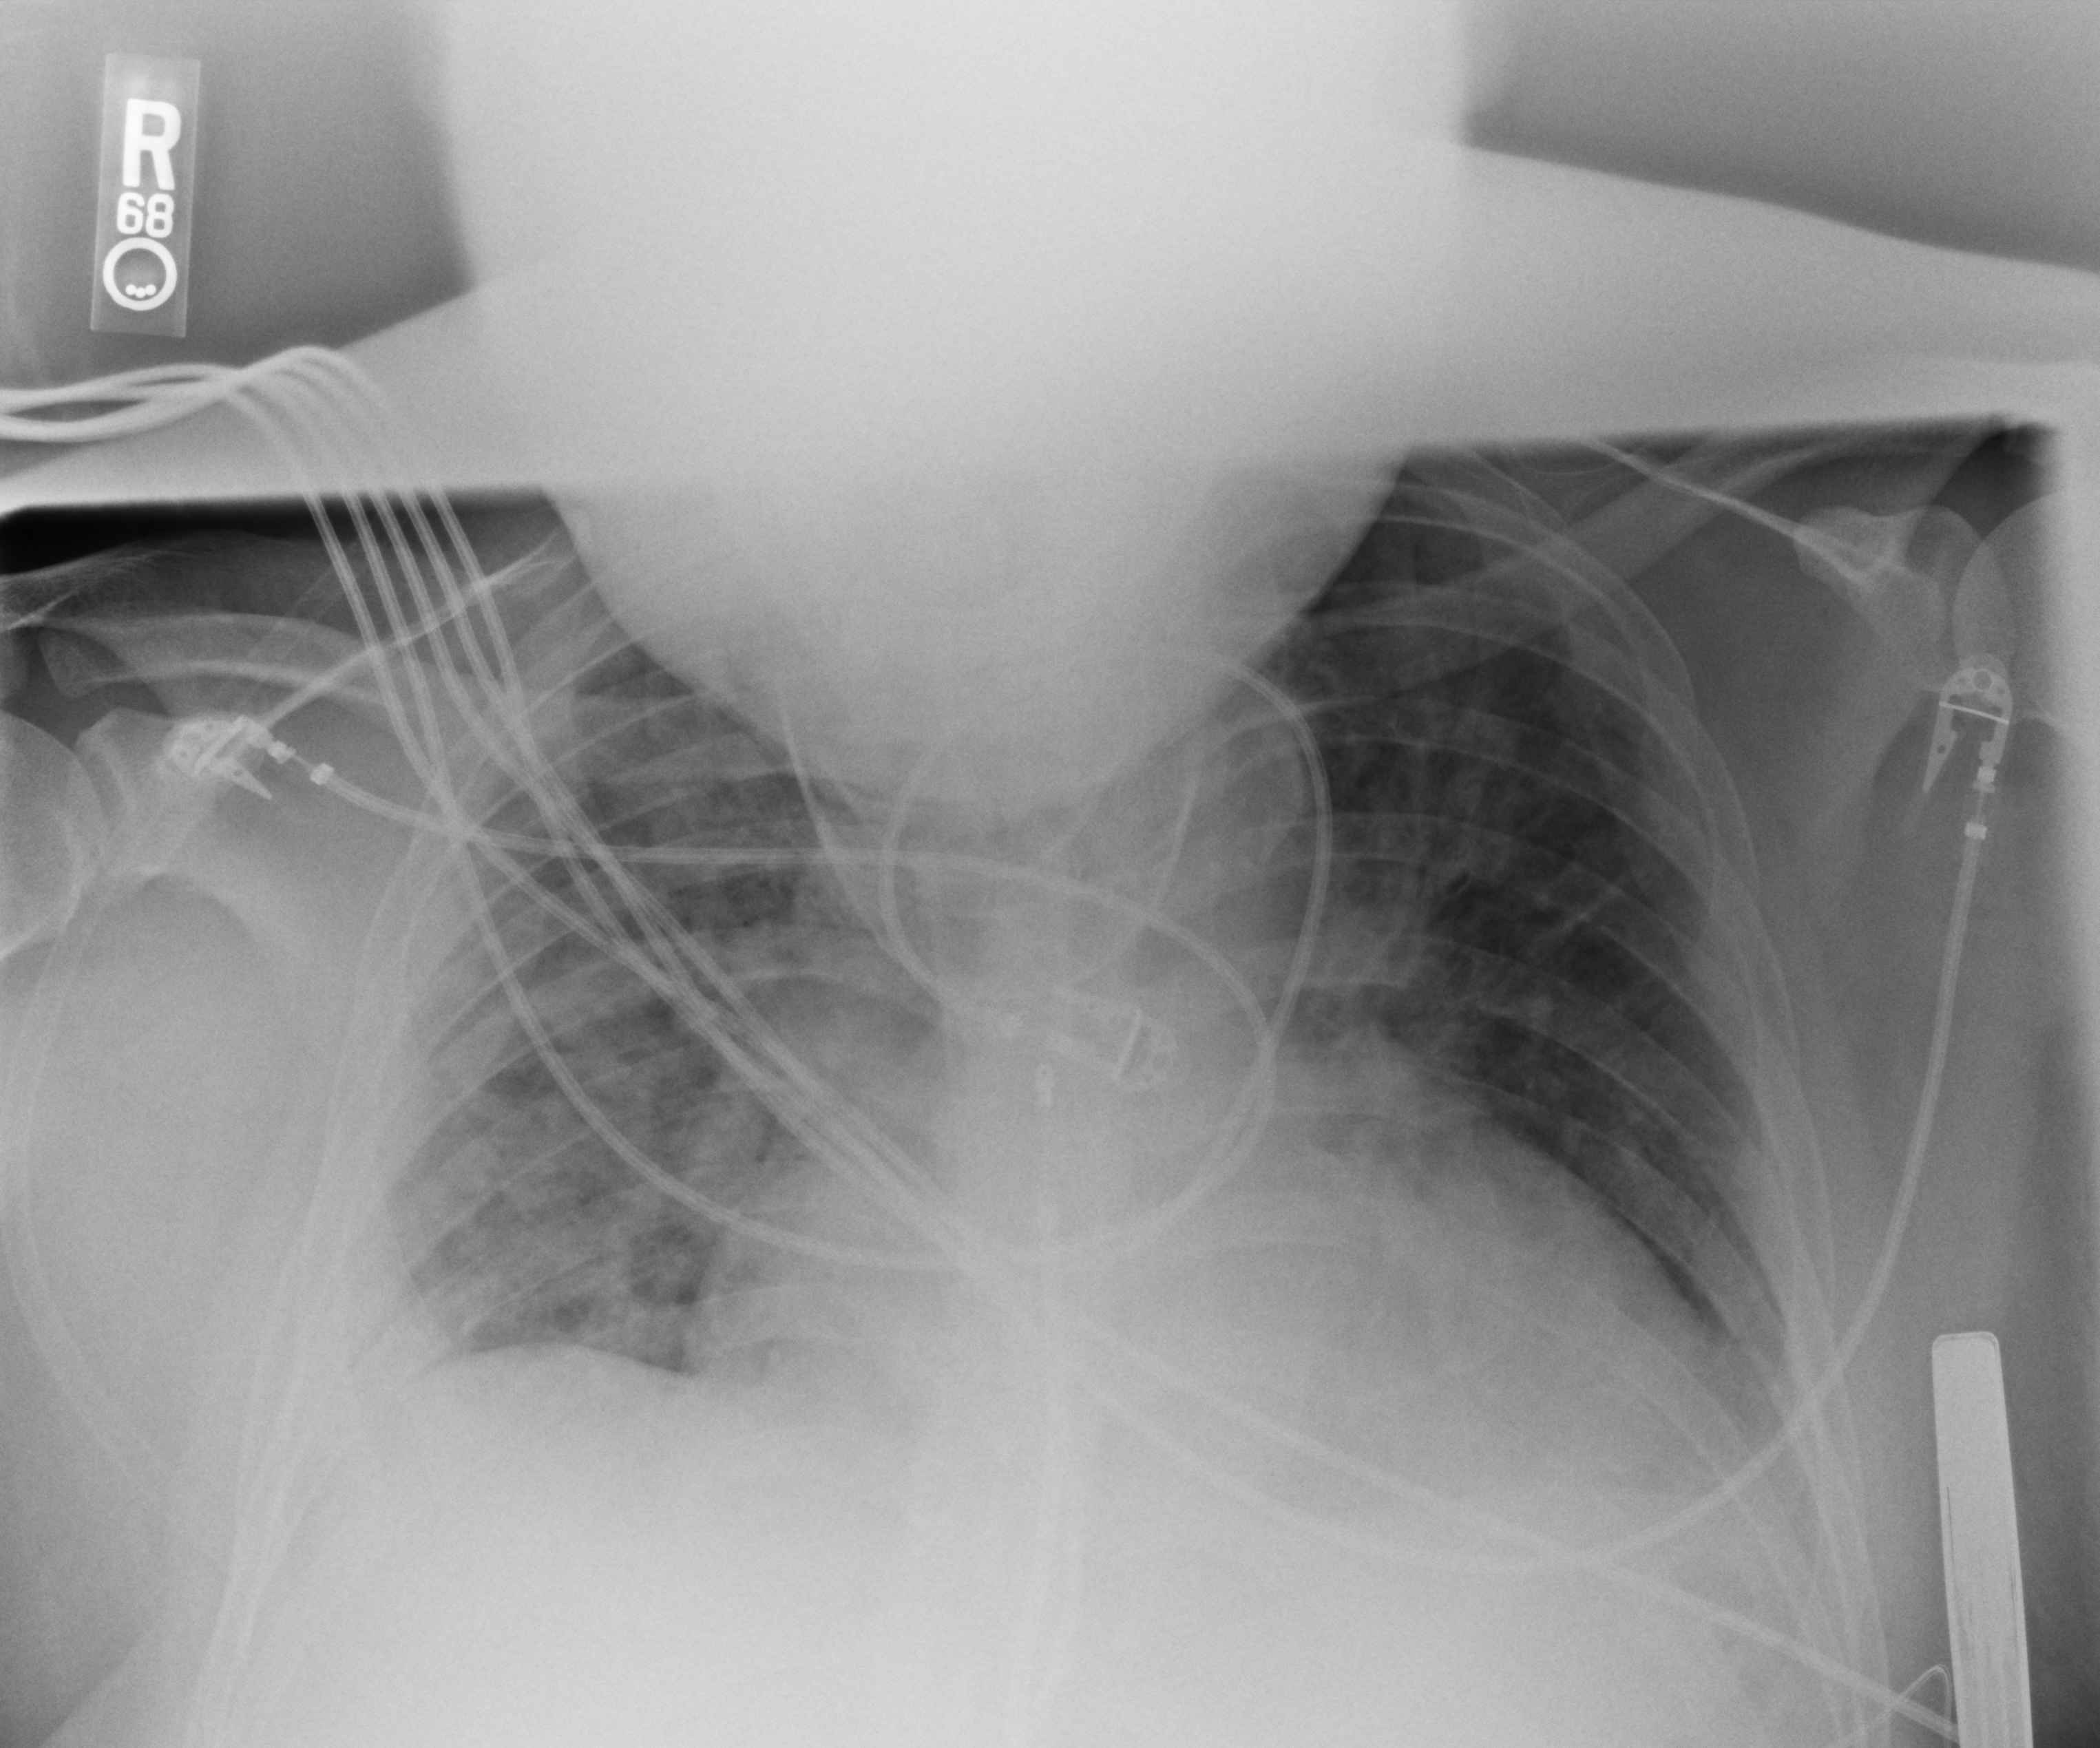
Chest X-ray (portable). Patient hospitalised with COVID-19; male, aged 18–59 years.
Hospital-stay facts (about this admission, not read from this image; timing relative to this image not recorded): COPD (admission record): no; admitted to intensive care during this hospital stay: no; mechanically ventilated during this hospital stay: no.